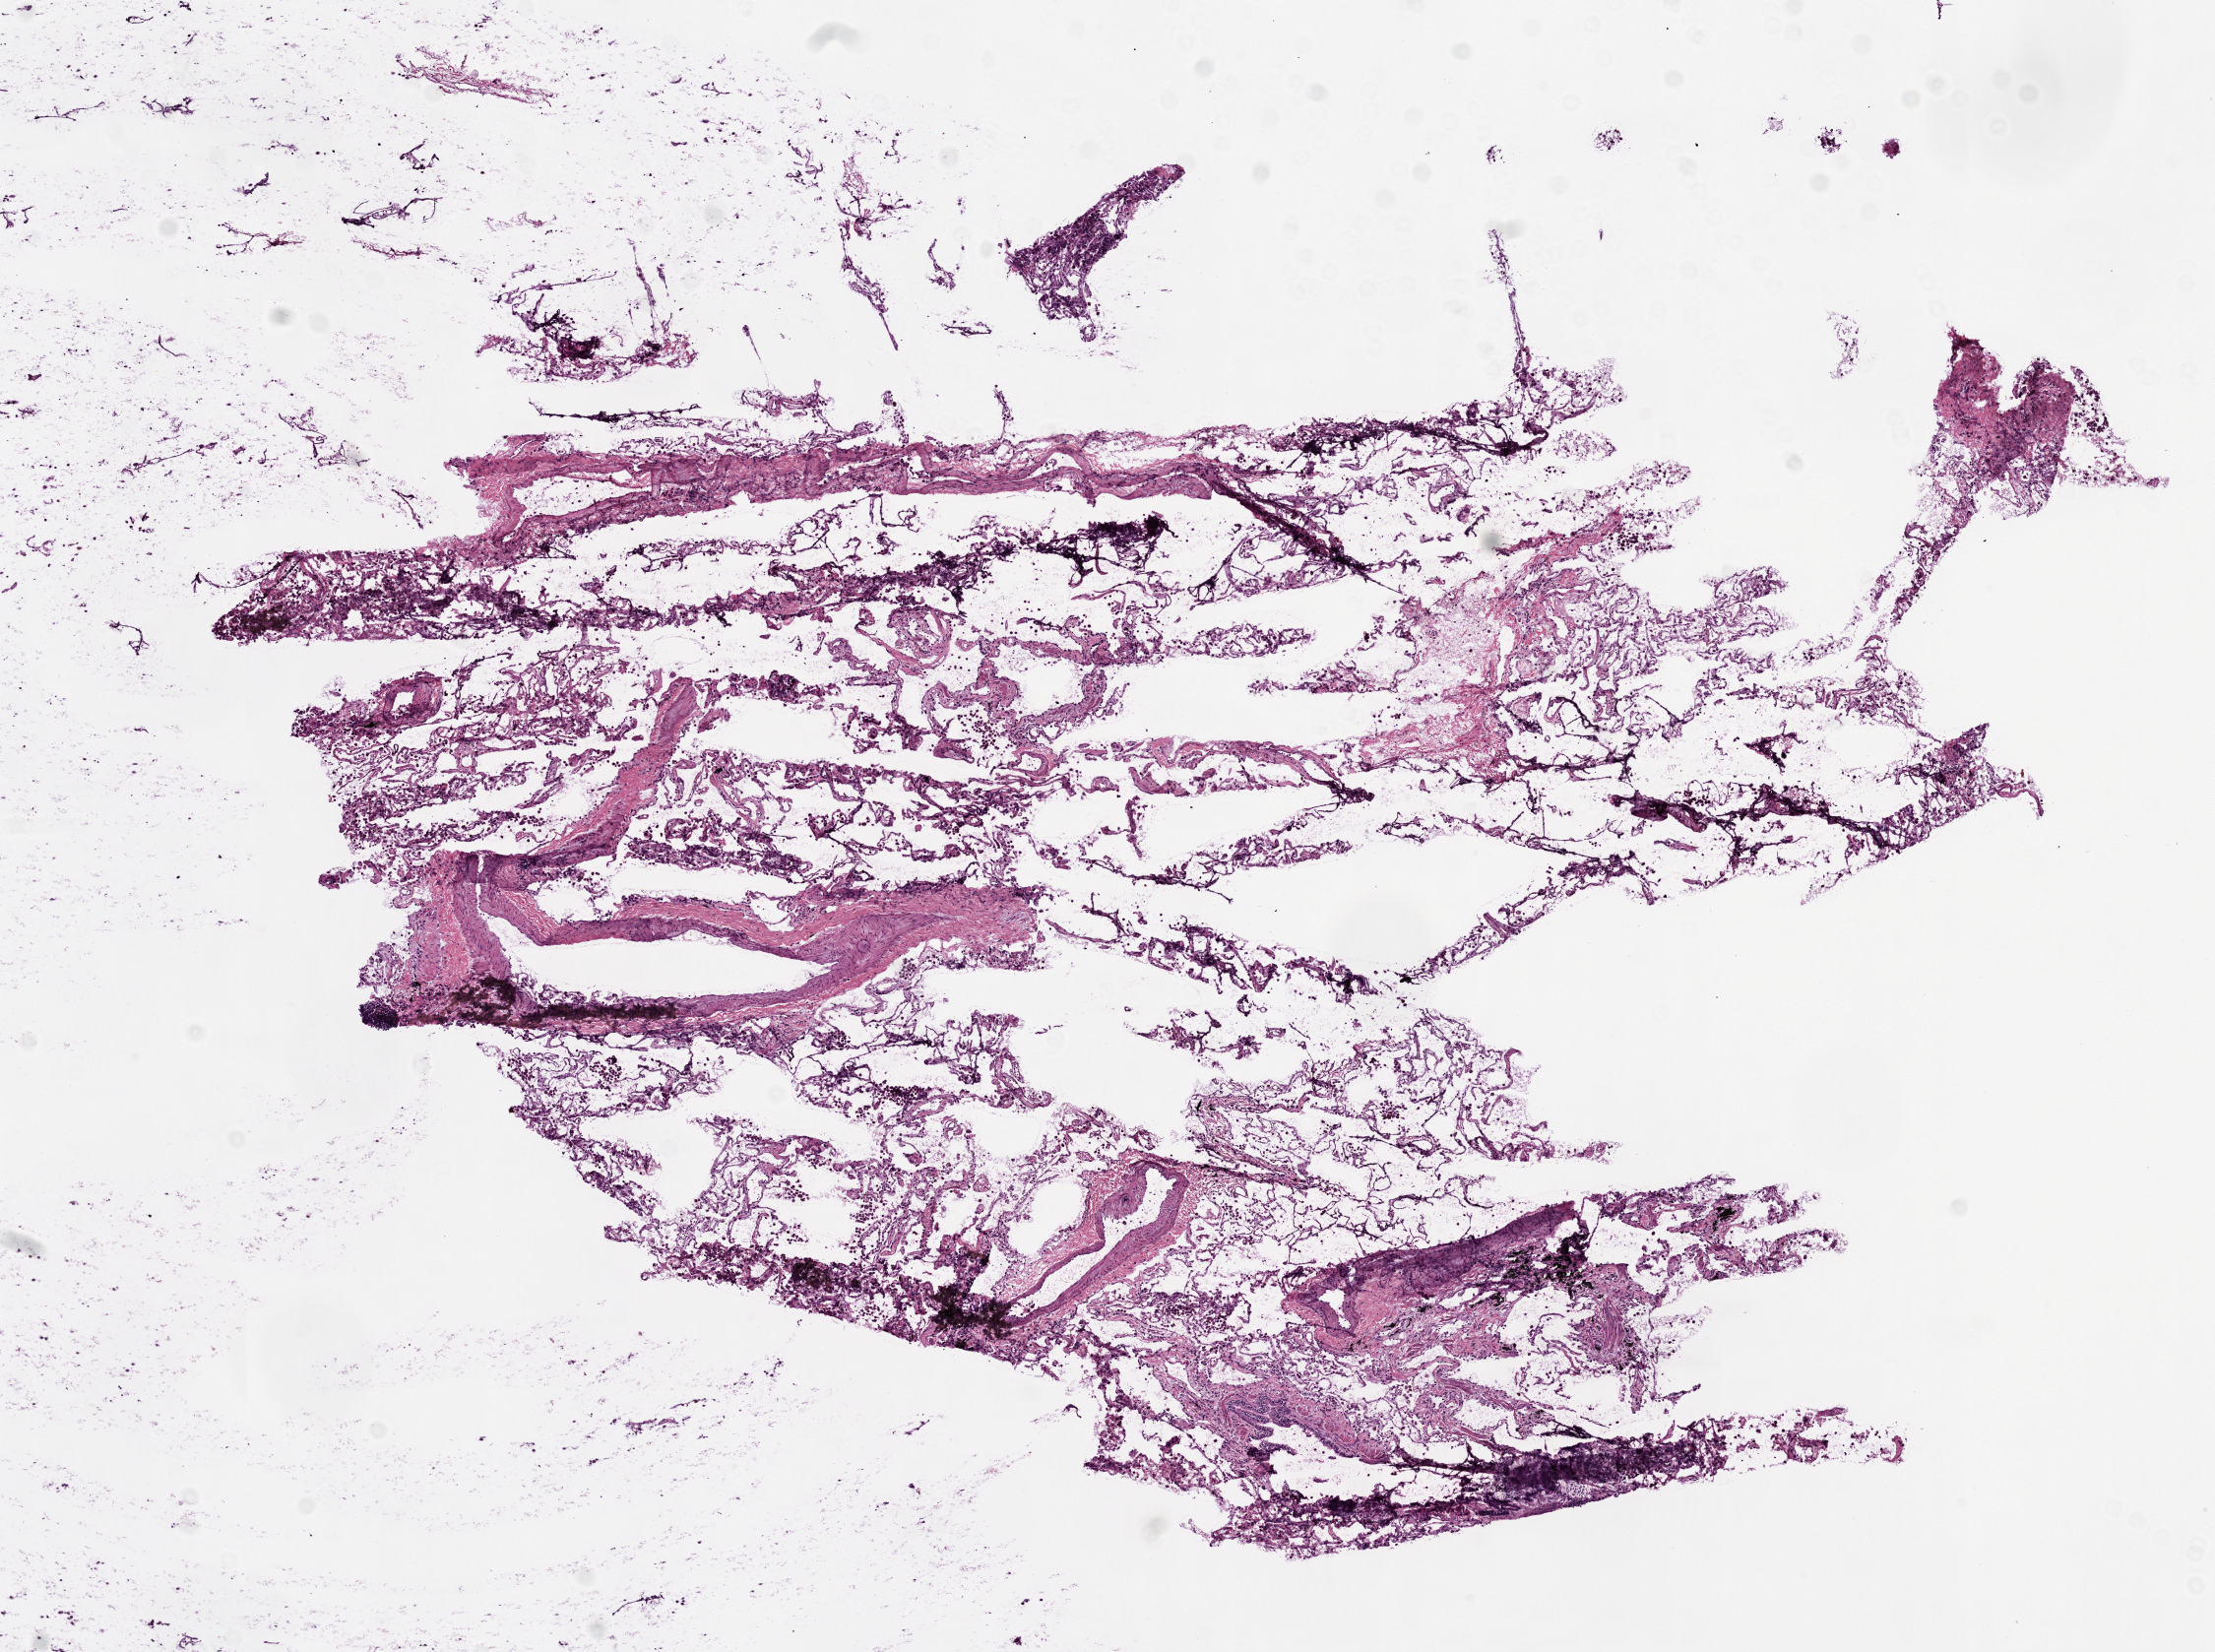
Hematoxylin and eosin (H&E) stained whole-slide image — a low-resolution overview of the entire scanned area, about 9.0 x 6.7 mm (acquisition: 20x scan); frozen section from the top of the tissue portion; sample: solid tissue normal (non-tumour tissue), lung. Male patient; age at initial diagnosis 58 years.
This section: solid tissue normal (non-tumour) sample from the same patient. Patient diagnosis: Squamous cell carcinoma, NOS.